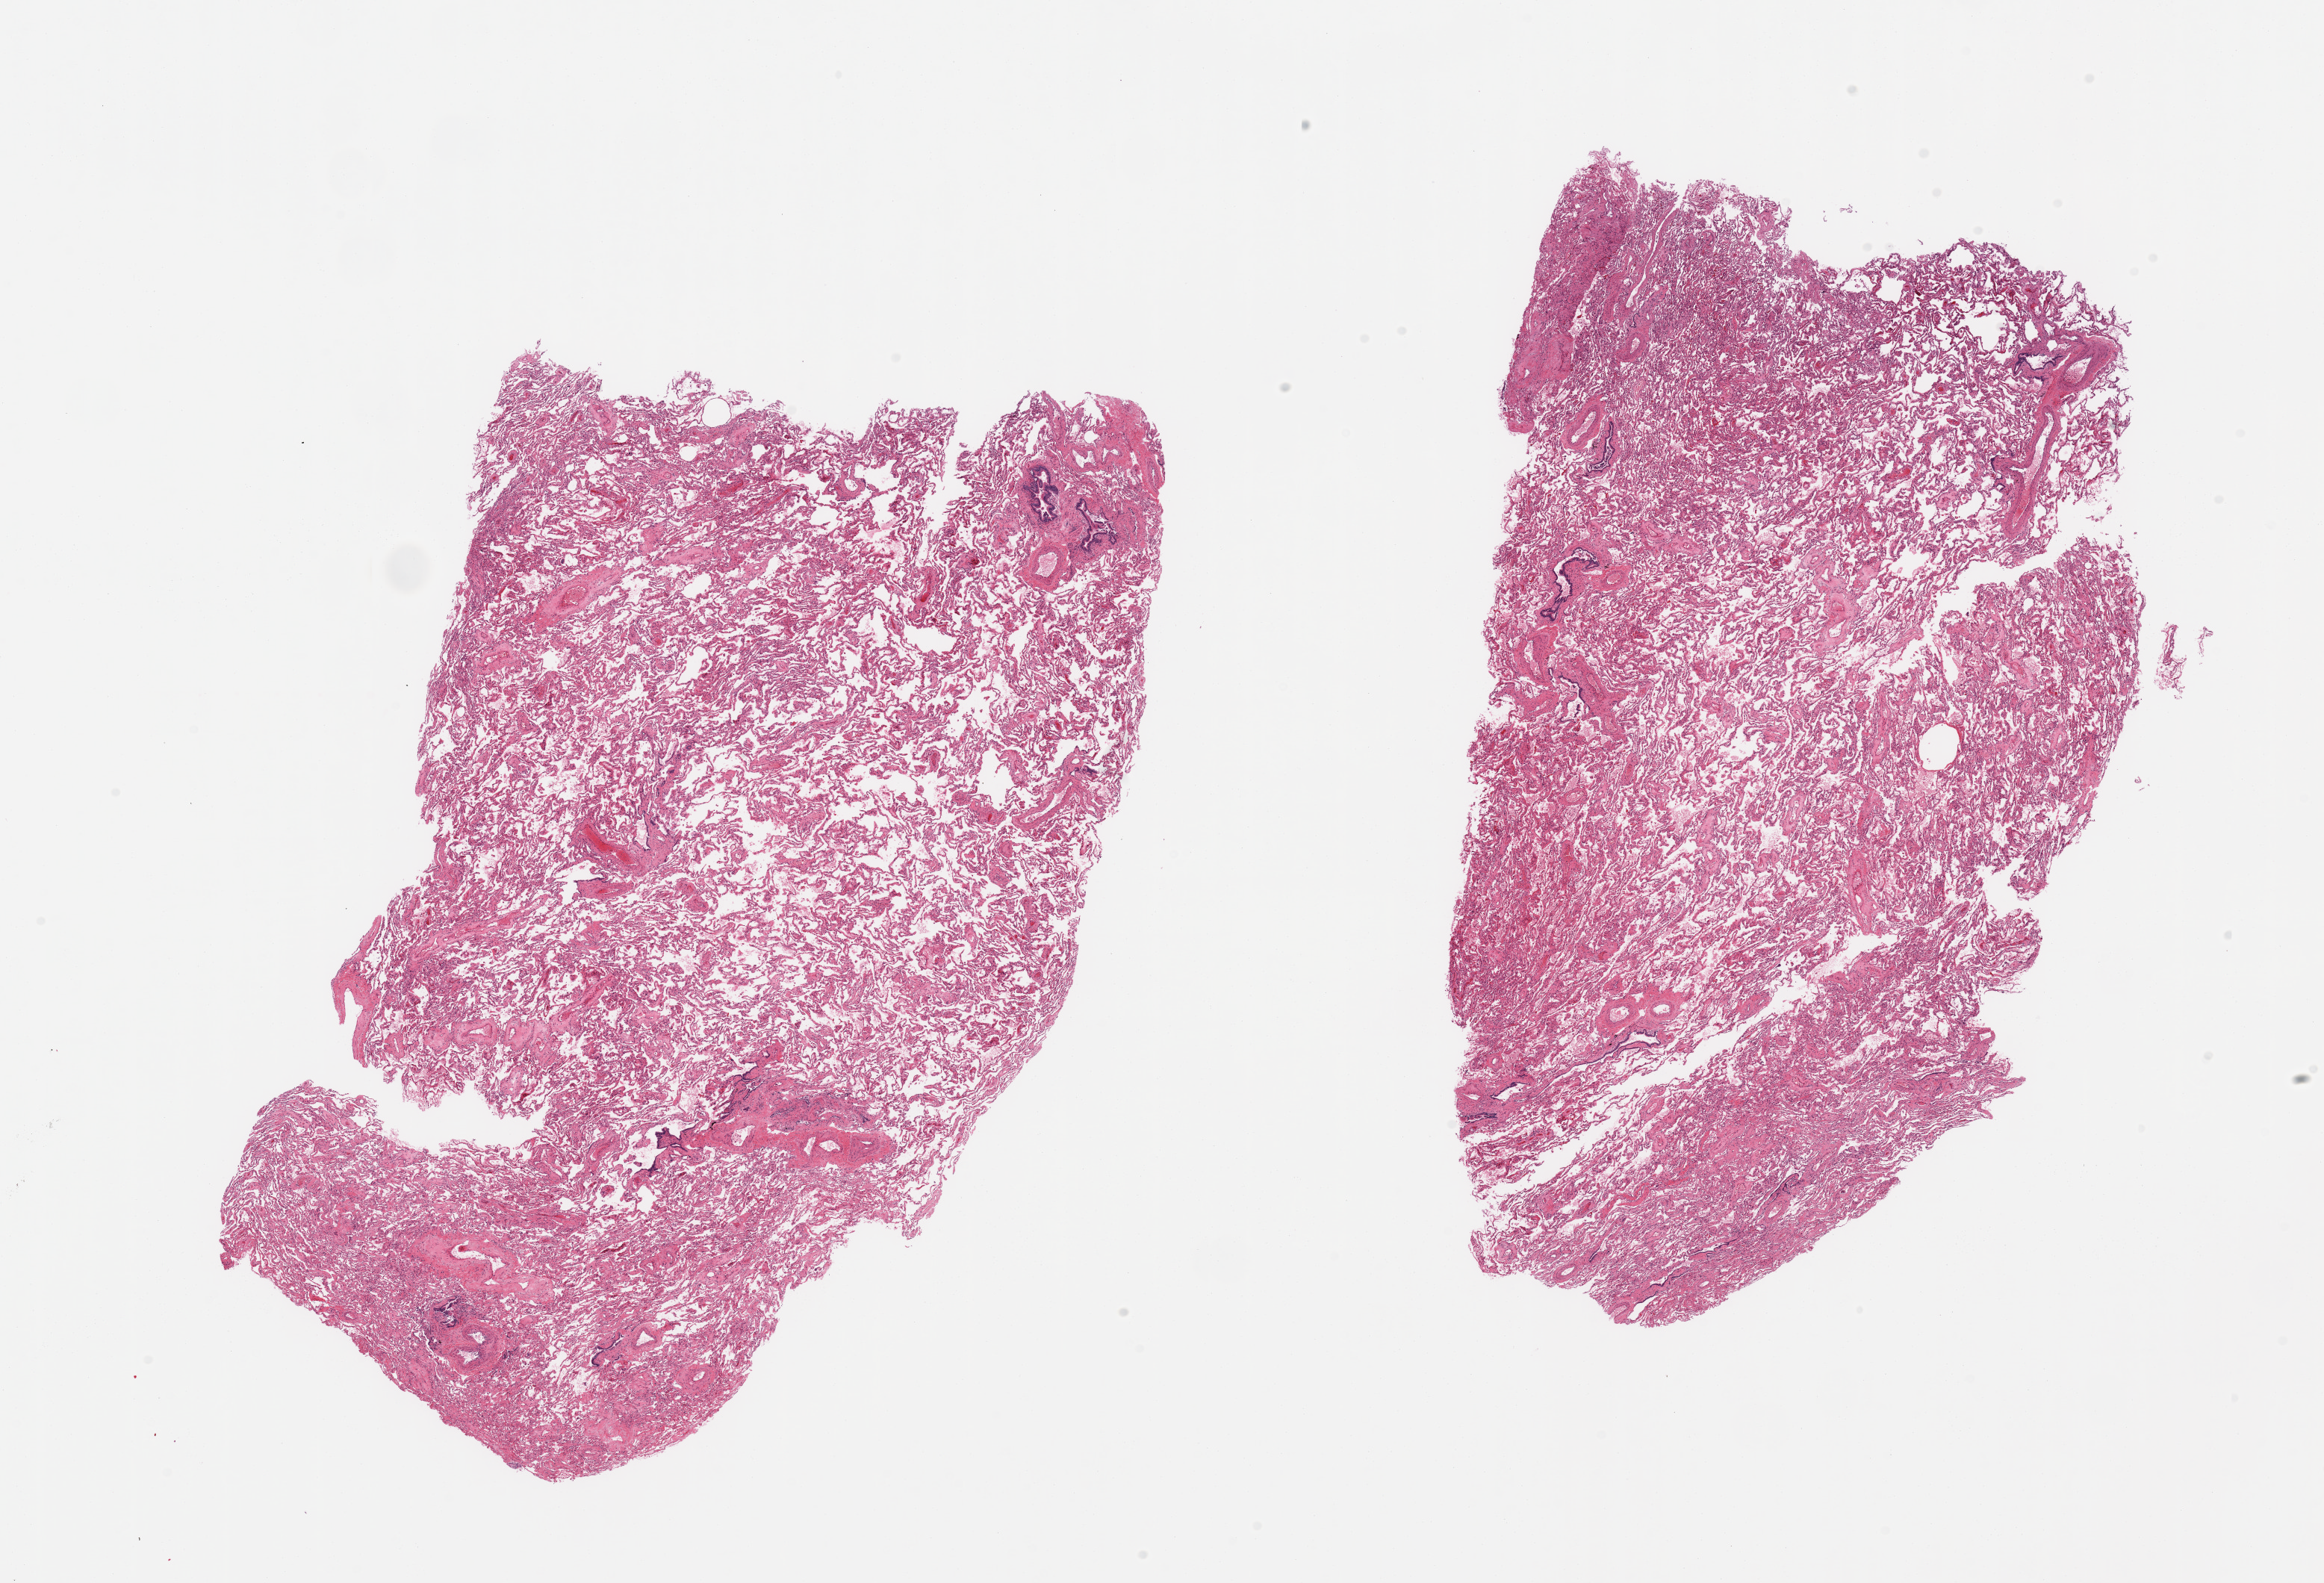
Whole-slide image, haematoxylin and eosin stain, whole scanned area (about 24.6 x 16.8 mm) shown as a low-resolution overview; PAXgene-fixed paraffin-embedded (PFPE) section; sampled site (target tissue): lung; donor tissue sample. Donor: male.
Reviewer comment on this tissue sample: 2 pieces, minimal congestion.